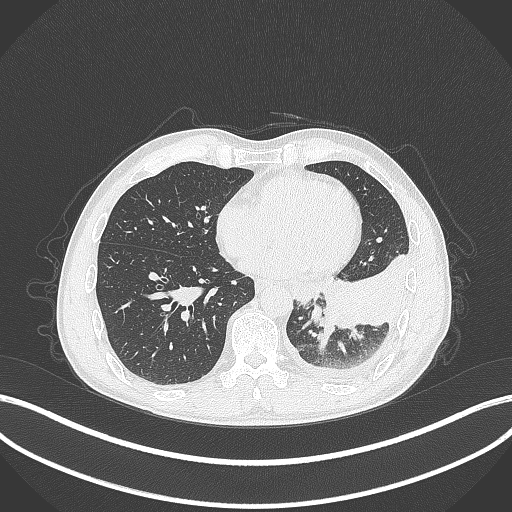
Chest CT, one axial slice. Position 102 of 295 along the scan axis. Lung window (W 1500 / L -600 HU). 1 mm slice thickness. 512 × 512 image matrix, field of view 400 × 400 mm. Patient: male, 47 years. From the clinical record (not read from this slice): clinical TNM (as recorded): T3 N1 M1c.
Structures marked on this image (rectangle marked by the reading radiologist):
- lung tumour (recorded histology: small cell carcinoma): bounding box <319,314,328,330> (left, top, right, bottom; pixels)